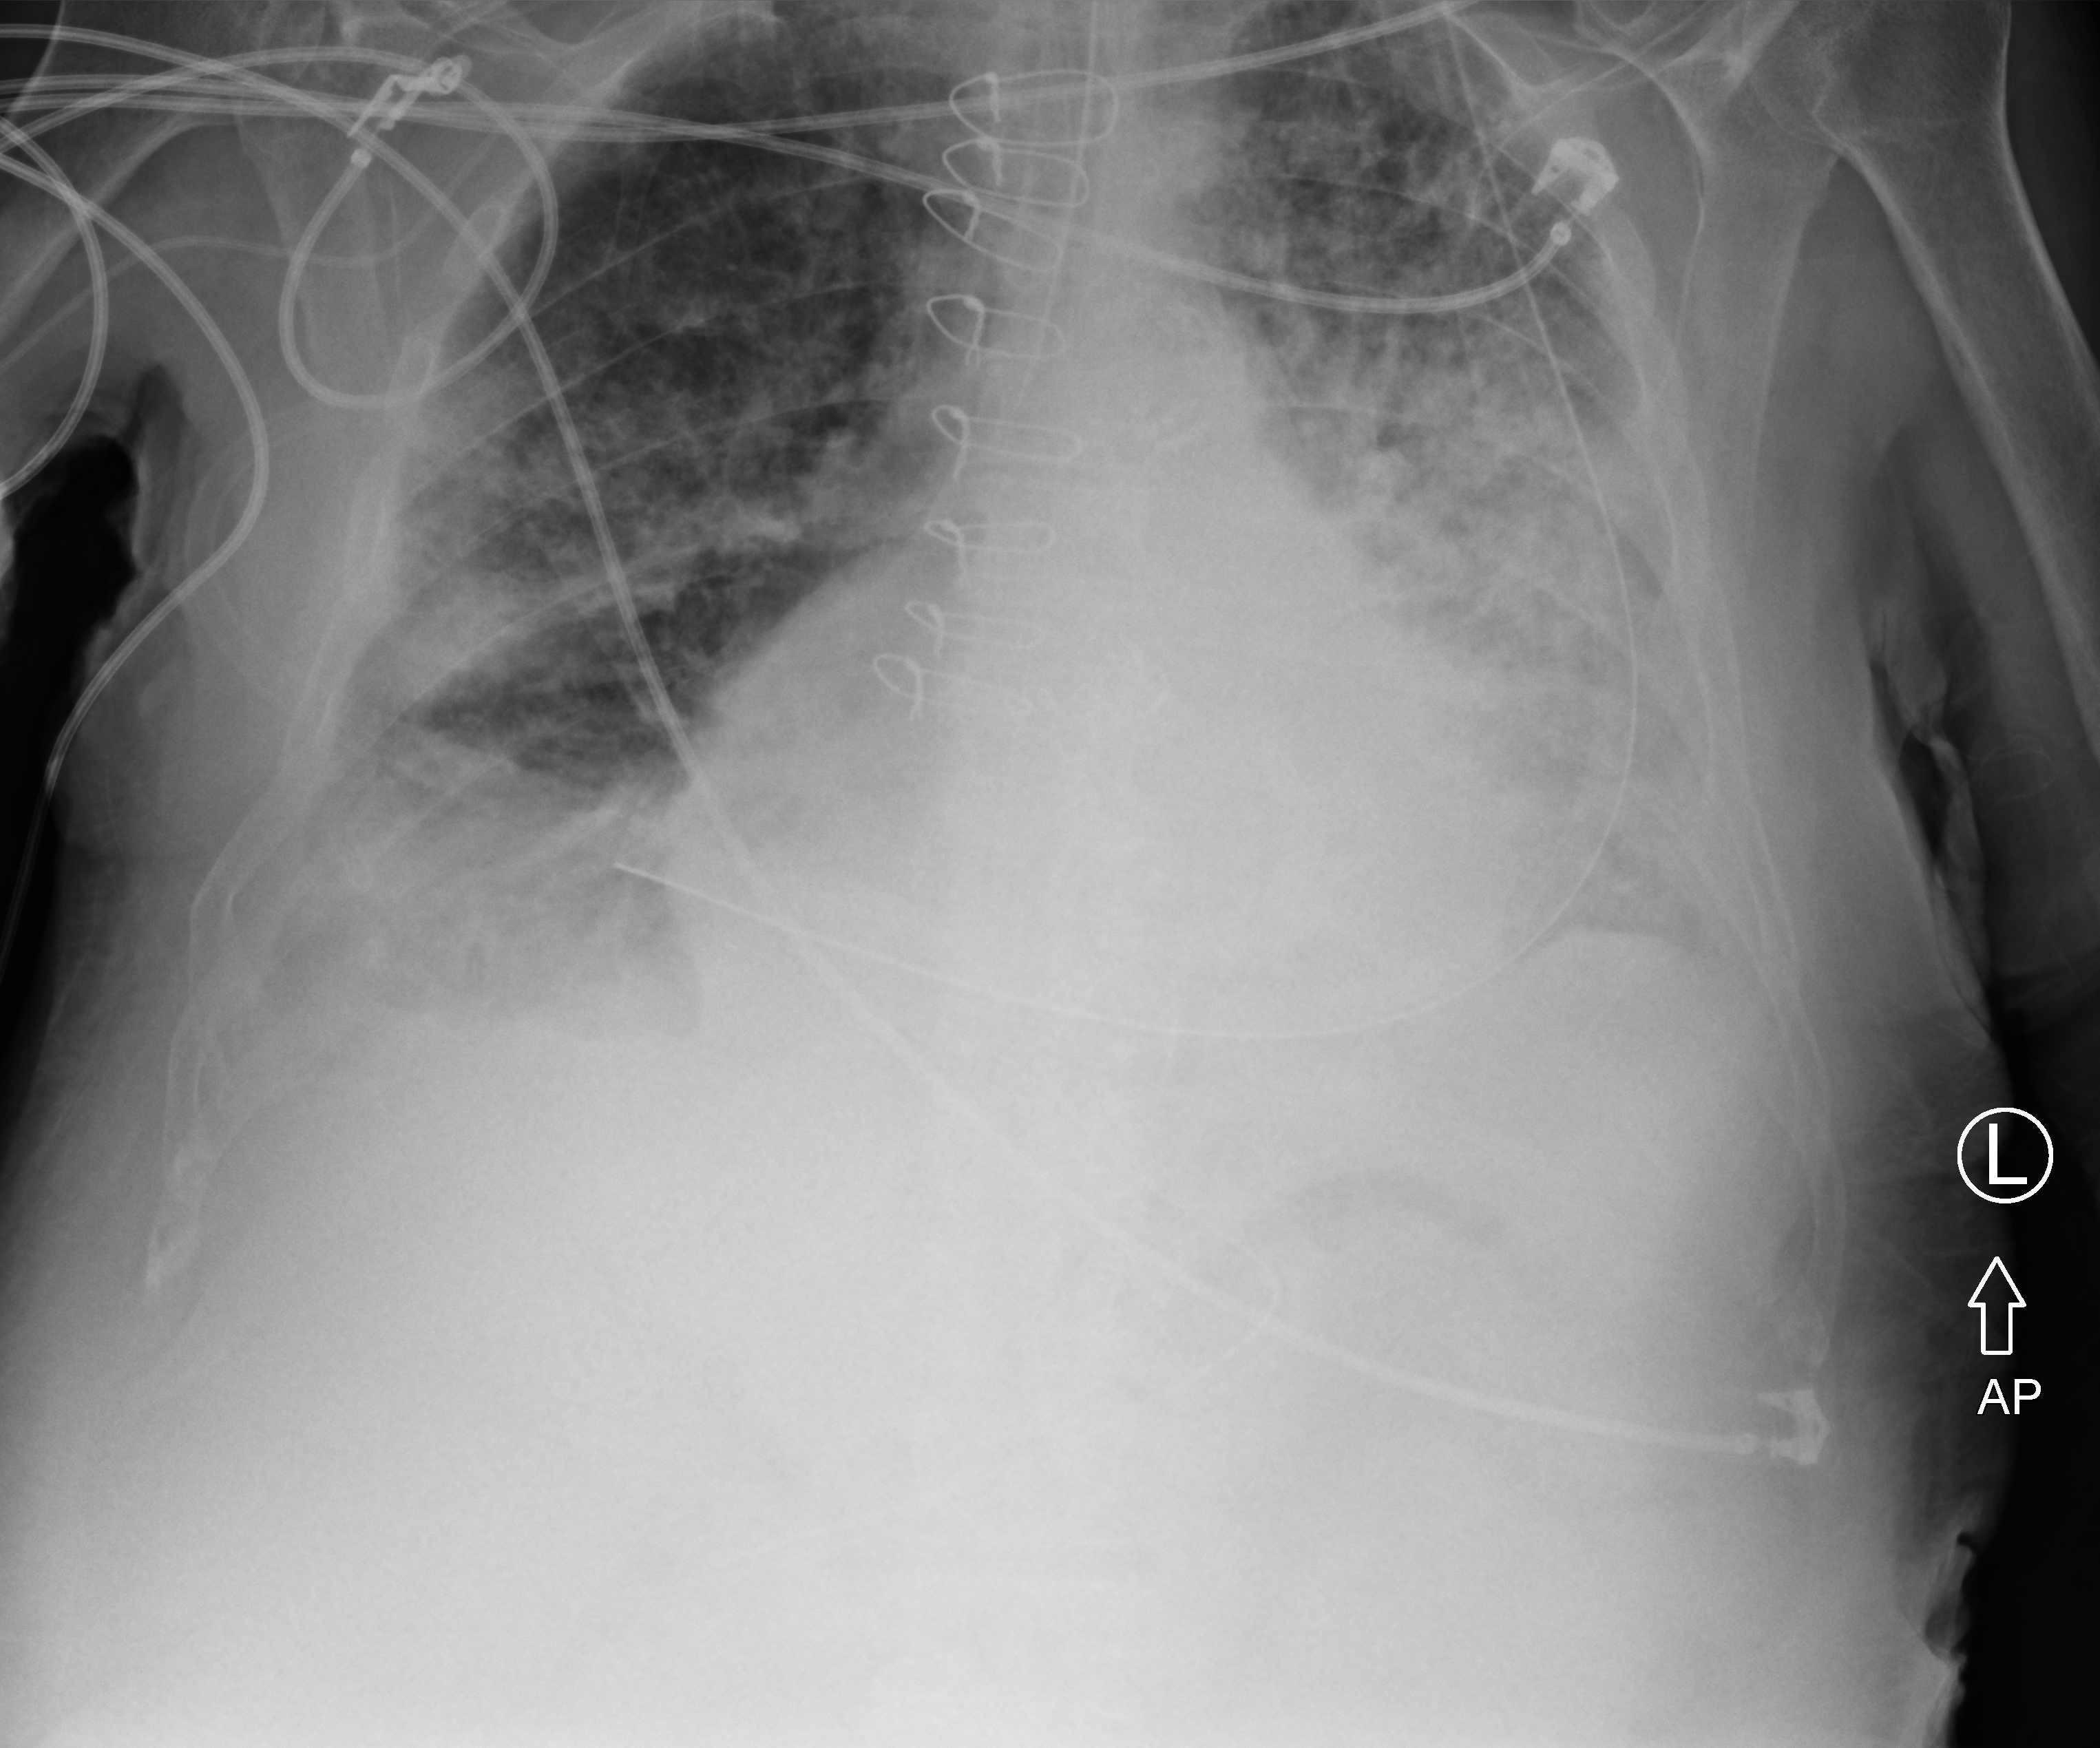
Chest X-ray (portable), anteroposterior (AP) projection. Patient hospitalised with COVID-19; male, aged 75–90 years.
From the hospital-stay record, not from the radiograph (when in the stay this image was taken is not recorded): admitted to intensive care during this hospital stay: yes.